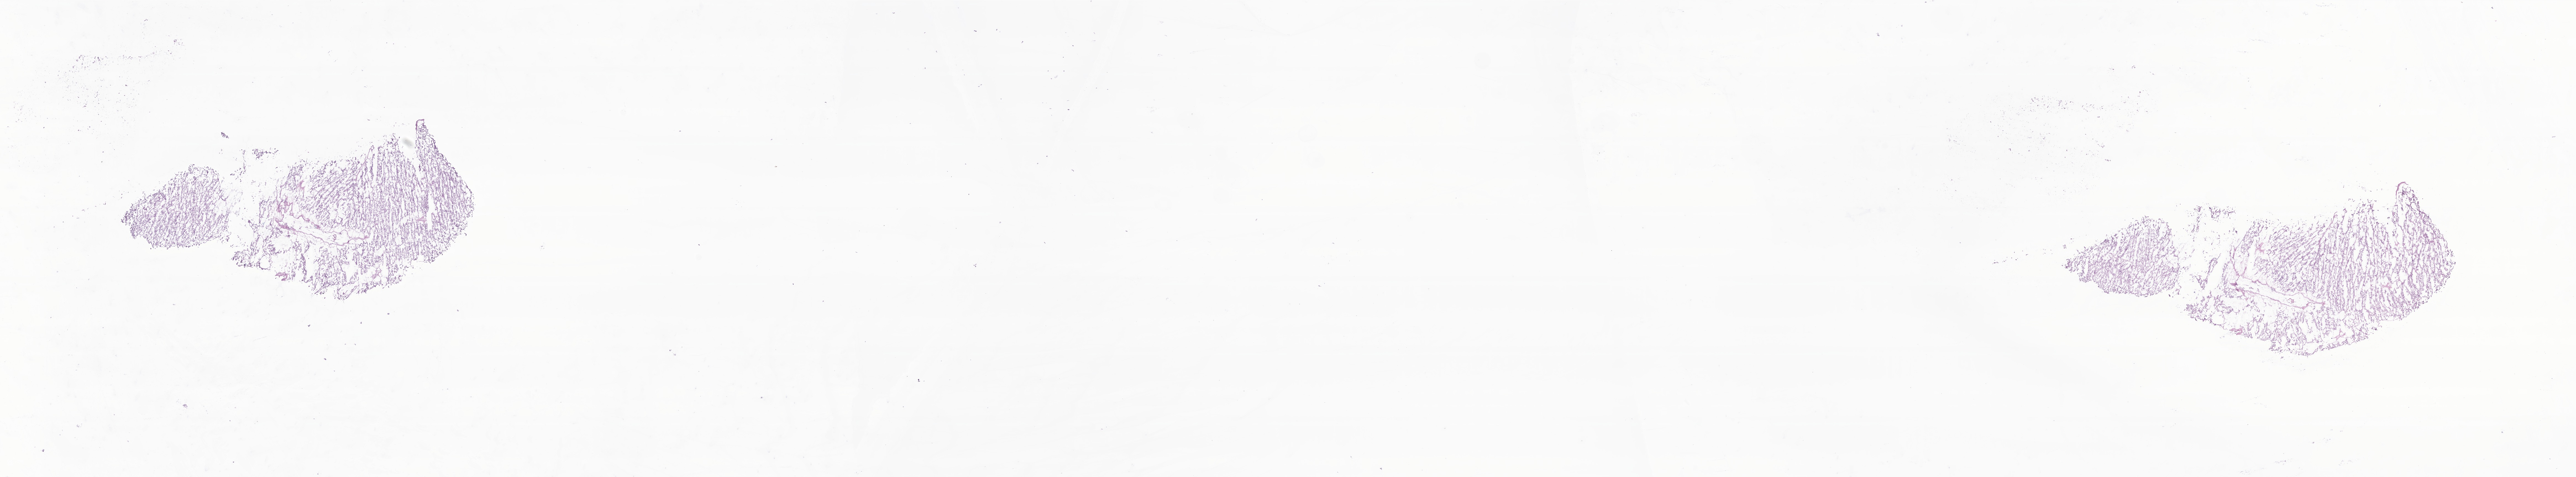
H&E whole-slide image of tumor tissue from the retroperitoneum, whole scanned area (about 39.3 x 7.3 mm) shown as a low-resolution overview. Female patient, age 231 months (19 years 3 months).
Specimen: frozen section (OCT-embedded).